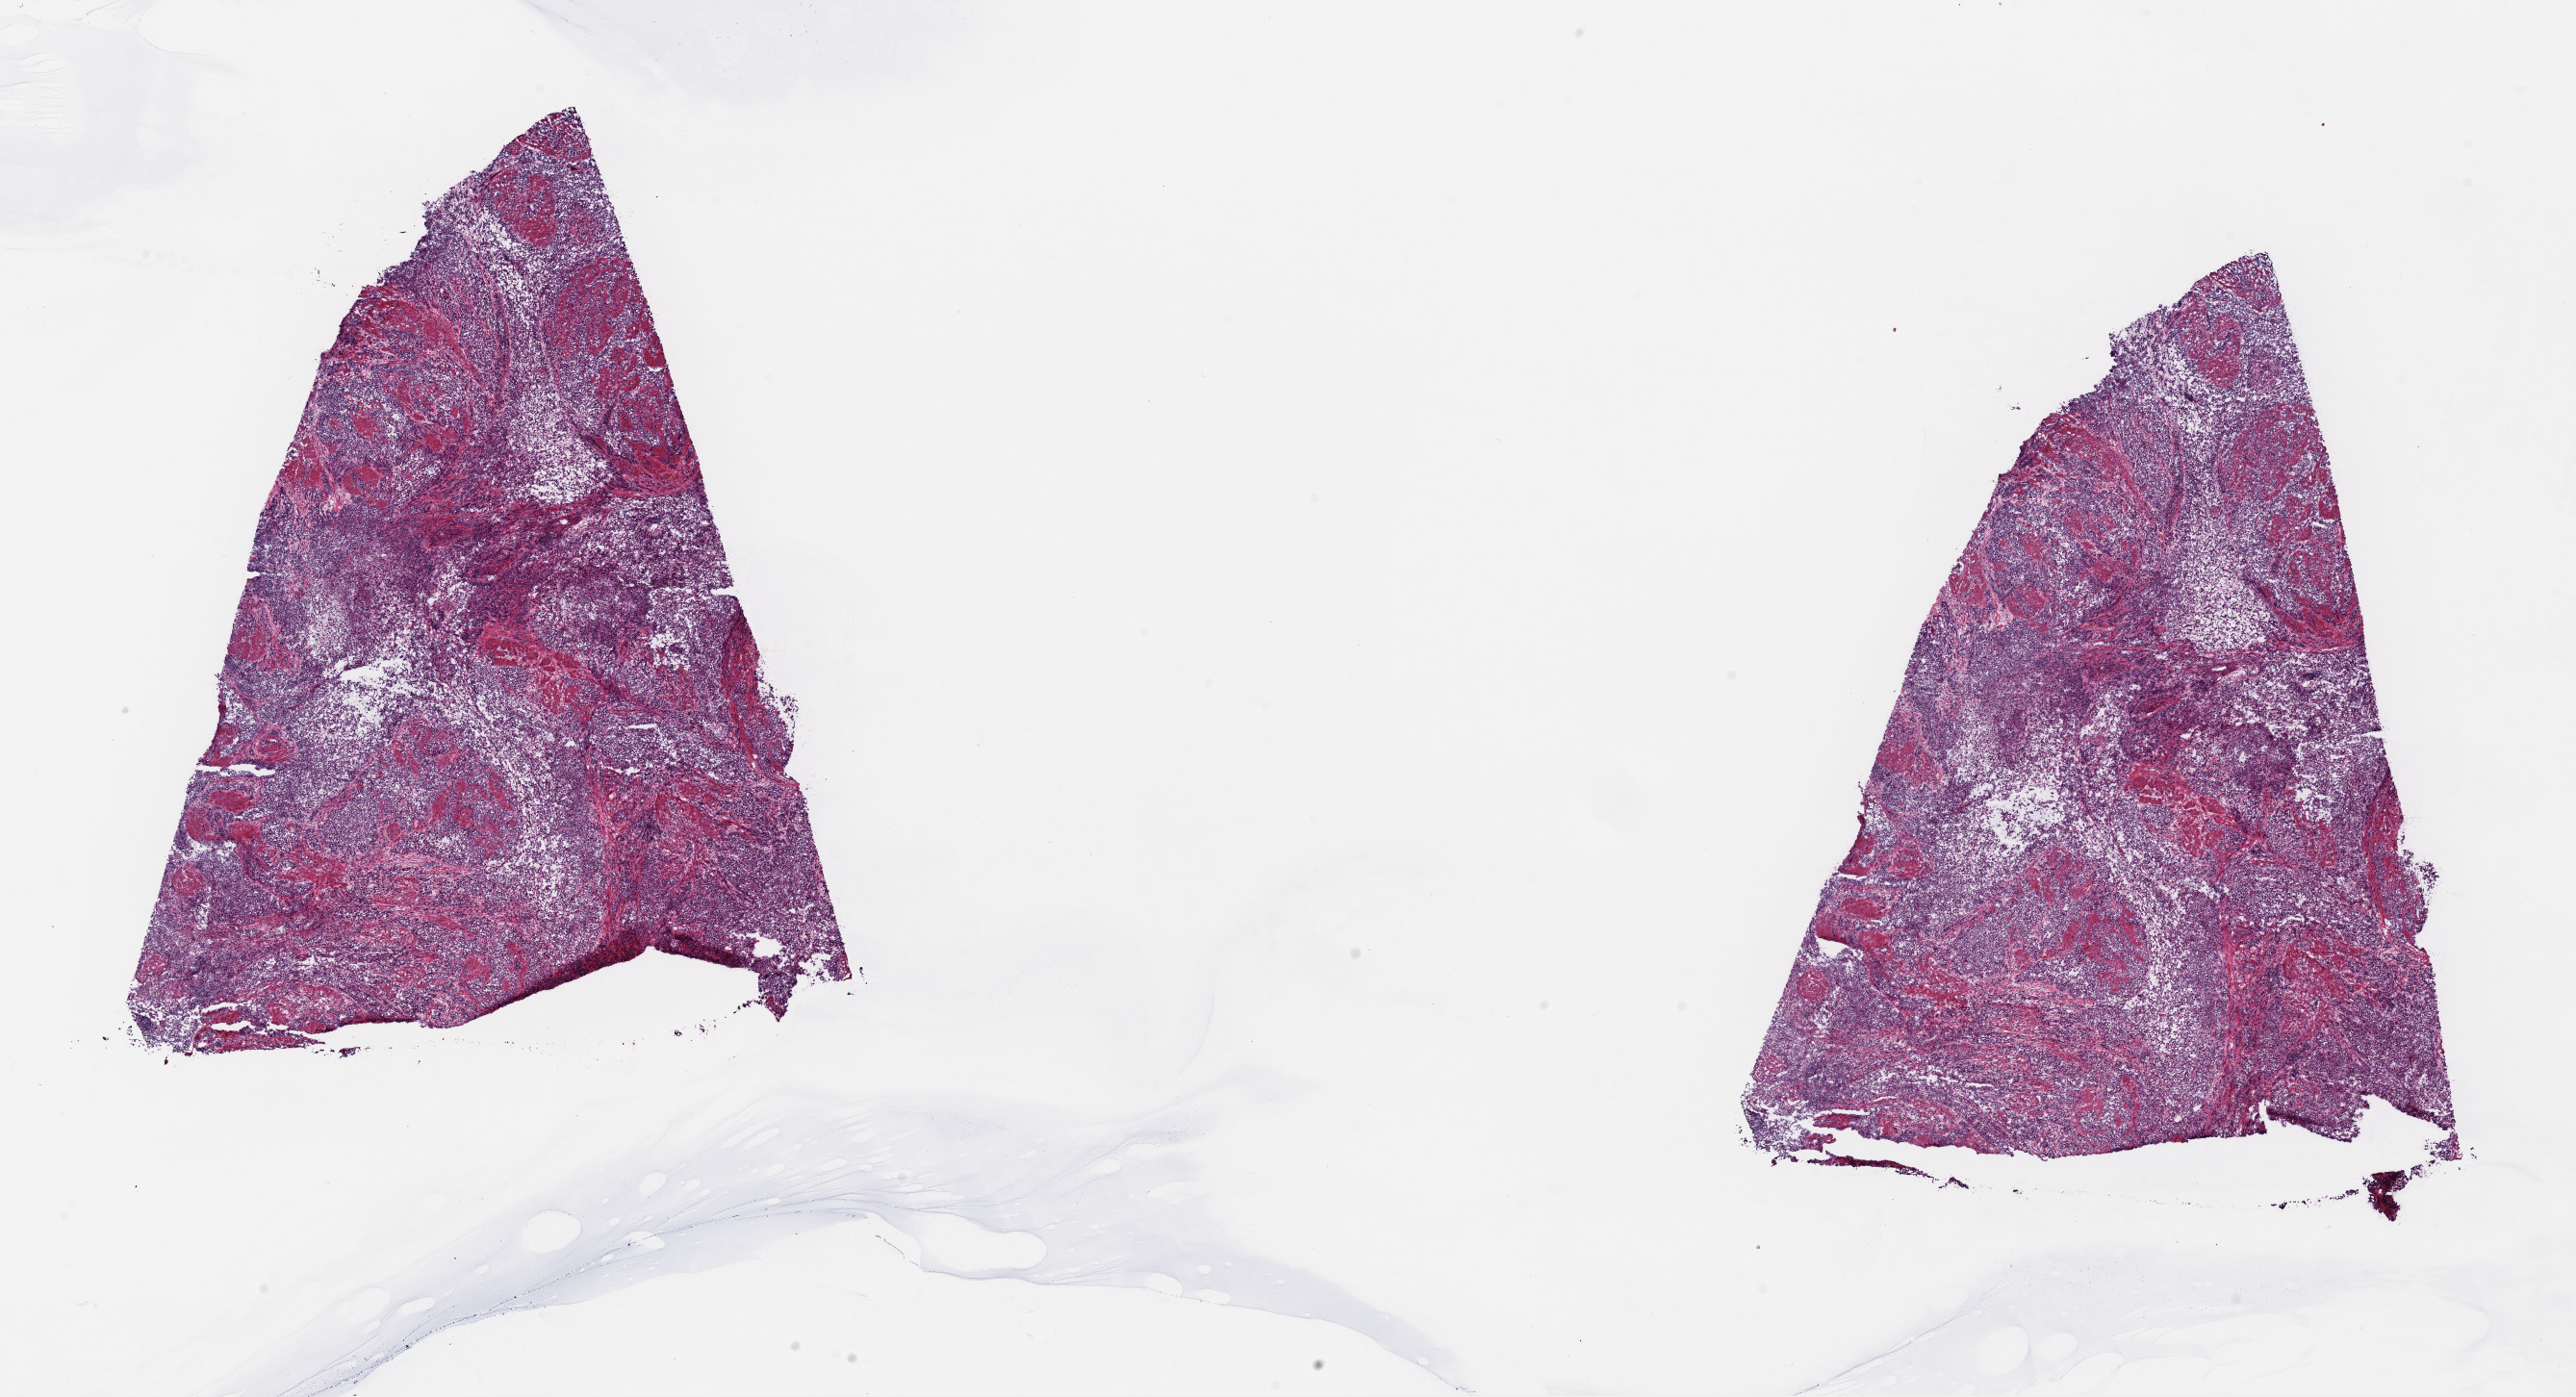
Hematoxylin and eosin (H&E) stained whole-slide image — low-resolution overview of the scanned area, about 21.1 x 11.5 mm (acquisition: 40x scan), frozen section from the top of the tissue portion, bladder, primary tumour sample. Patient: male, age at initial diagnosis 73 years. Histologic grade: high grade. Composition of this section per pathologist review: tumour cells 100%, tumour nuclei 80%, normal cells 0%, stromal cells 0%, necrosis 0%. Inflammatory infiltration, as recorded: lymphocyte infiltration 0%, monocyte infiltration 0%, neutrophil infiltration 0%.
Lymph nodes positive (case pathology): 4 of 23 examined. AJCC pathologic stage: IV (6th edition). Histologic diagnosis: Transitional cell carcinoma.